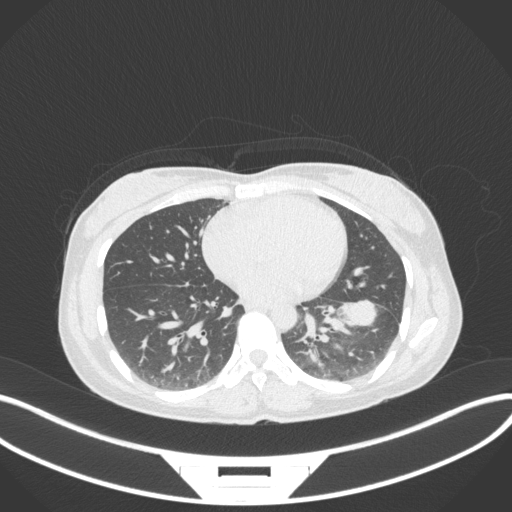
Chest CT, one axial slice; slice 148 of 361 in the series (ordered by position); reconstruction kernel B31f; lung window (W 1500 / L -600 HU); 512 × 512 image matrix. Patient: female, 41 years. Case-level facts recorded for this patient, not image findings: clinical TNM (as recorded): T2a N3 M1b.
Structures marked on this image (rectangle marked by the reading radiologist):
- lung tumour (recorded histology: adenocarcinoma): bounding box [x1, y1, x2, y2] px = [334, 292, 386, 328]